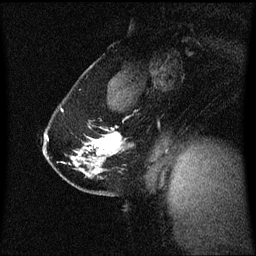
Breast MRI (dynamic contrast-enhanced), one sagittal slice. Position 41 of 60 along the scan axis. Dynamic contrast-enhanced series, image 2 of 3 at this slice position (ordered by acquisition). 1.5 T. TE 4.2 ms, TR 8.4 ms. 2 mm slice thickness. 256 × 256 image matrix, field of view 210 × 210 mm. Patient: female, 40 years. From the clinical record (not read from this slice): setting: breast cancer imaged before/during neoadjuvant chemotherapy; receptor status: triple-negative.
Outlined on this slice (semi-automatically segmented with operator editing):
- analysis volume of interest (the breast-tissue region the enhancement analysis was run in; not a lesion): bounding box [x1, y1, x2, y2] px = [44, 127, 122, 187]
- tumour enhancement mask (voxels above the 70 % enhancement threshold inside the analysis volume of interest): [94, 134, 122, 151]